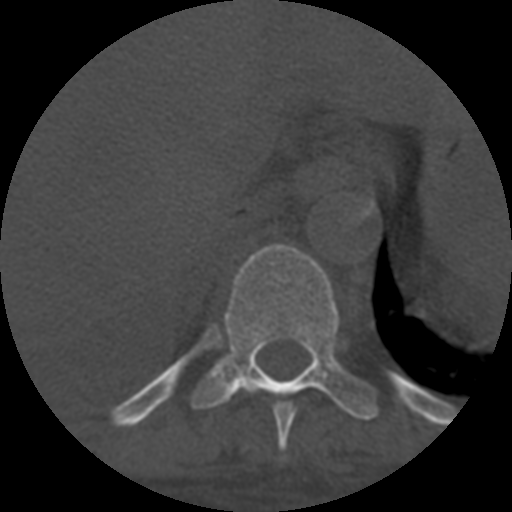
CT including the spine, one axial slice; slice 362 of 708 in the series (ordered by position); reconstruction kernel STANDARD; 120 kVp; one of 3 acquisitions stored at this slice position; bone window (W 1800 / L 400 HU); 1.25 mm slice thickness; 512 × 512 image matrix. Patient age 55 years. Case-level facts recorded for this patient, not image findings: primary cancer: colon; vertebrae with lytic lesions (as recorded): T12, L1, L5.
Outlined on this slice (semi-automatic segmentation, software-assisted and operator-edited):
- T10 vertebra: bounding box <190,244,378,420> (left, top, right, bottom; pixels)
- T9 vertebra: <273,402,295,458>